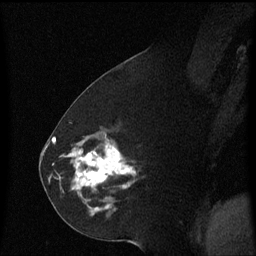
Breast MRI (dynamic contrast-enhanced), one sagittal slice. Position 29 of 60 along the scan axis. Dynamic contrast-enhanced series, image 2 of 3 at this slice position (ordered by acquisition). 1.5 T. TE 4.2 ms, TR 8.4 ms. 256 × 256 image matrix, field of view 200 × 200 mm. Female patient, age 60 years. From the clinical record (not read from this slice): setting: breast cancer imaged before/during neoadjuvant chemotherapy; receptor status: triple-negative.
Structures marked on this image (semi-automatically segmented with operator editing):
- analysis volume of interest (the breast-tissue region the enhancement analysis was run in; not a lesion): box from (x=70, y=142) to (x=136, y=215) px
- tumour enhancement mask (voxels above the 70 % enhancement threshold inside the analysis volume of interest): (x=70, y=142)–(x=136, y=189)